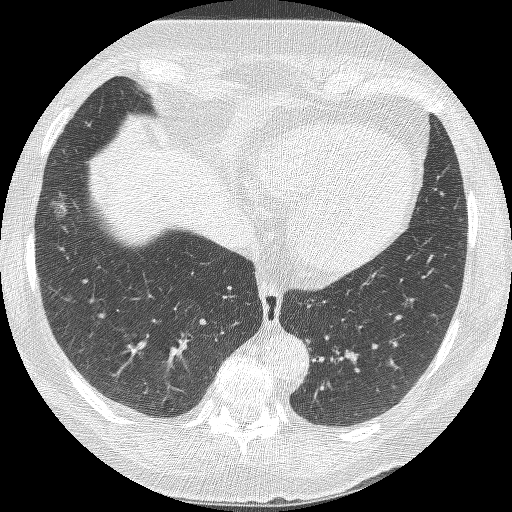
Axial slice from a low-dose chest CT screening exam; second annual screen; lung window (W 1500 / L -600 HU); 1.25 mm slice thickness; slice 87 of 245 in the series; 512 × 512 image matrix. Female participant, aged 68 years at enrolment.
Lesion marked by an expert reader, bounding box (x1, y1, x2, y2) in pixels: (36, 190, 77, 240). Screening reader's record for this exam (one nodule recorded; not confirmed to be the boxed lesion): non-calcified nodule or mass ≥4 mm, right lower lobe, 18 × 15 mm, poorly defined margins, ground glass attenuation, pre-existing on the prior screen: yes; interval growth: yes. Lung cancer was diagnosed 42 days after this screen: bronchiolo-alveolar adenocarcinoma, NOS, right lower lobe, well differentiated (G1), stage IA (AJCC 6th edition), 13 mm at pathology.